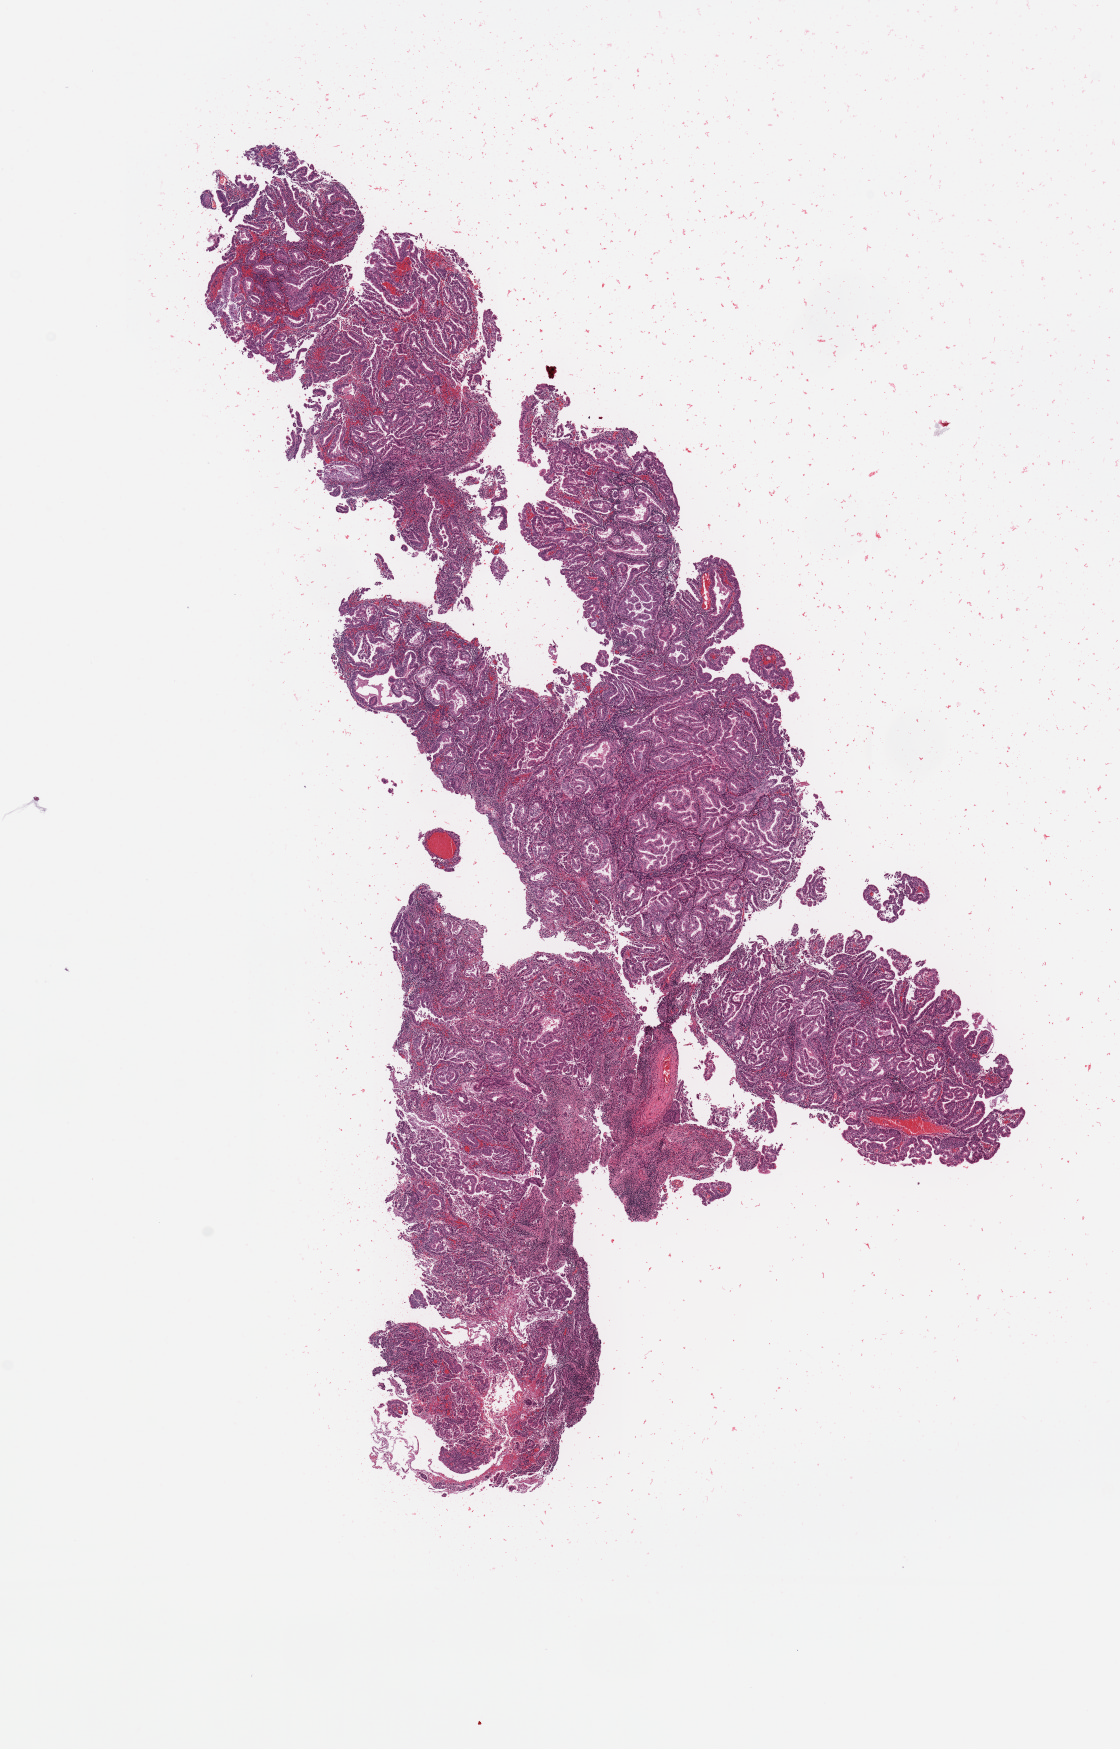
H&E-stained whole-slide image — shown as a low-resolution overview of the whole scanned area (about 8.9 x 13.8 mm, from a 20x scan). Tumour tissue sample, sampled site: uterus. Patient: female, age 42 years. Histologic grade: G1 (well differentiated). Slide review estimates, as recorded: tumour nuclei 90%, necrosis 0%.
Diagnosis: Endometrioid adenocarcinoma, NOS.